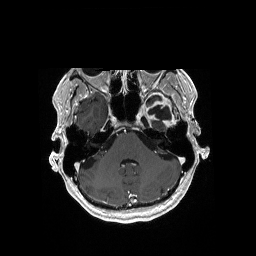
Brain MRI from a brain-tumour surgery series, one axial slice. Position 133 of 176 along the scan axis. T1-weighted post-contrast. 256 × 256 image matrix, field of view 256 × 256 mm. From the clinical record (not read from this slice): histopathology: Glioblastoma; WHO grade: 4; IDH mutation: no; tumour location: Left Medial Temporal.
Structures marked on this image (outlined manually by an expert reader):
- previous resection cavity: bounding box <148,105,171,120> (left, top, right, bottom; pixels)